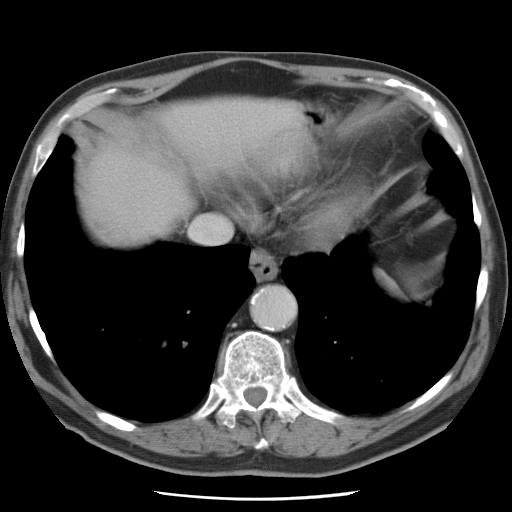
Contrast-enhanced abdominal CT, one axial slice; slice 71 of 78 in the series (ordered by position); 120 kVp; soft-tissue window (W 400 / L 40 HU); 512 × 512 image matrix, field of view 337 × 337 mm. Male patient, age 75 years. Case-level facts recorded for this patient, not image findings: diagnosis: colorectal cancer liver metastases, imaged before liver resection; multiple liver metastases: yes; largest metastasis: 2.4 cm; disease in both lobes: yes.
Structures marked on this image (manually delineated by an expert):
- liver: bounding box [x1, y1, x2, y2] px = [88, 97, 293, 241]
- planned liver remnant (the part of the liver to remain after resection): [89, 162, 171, 240]